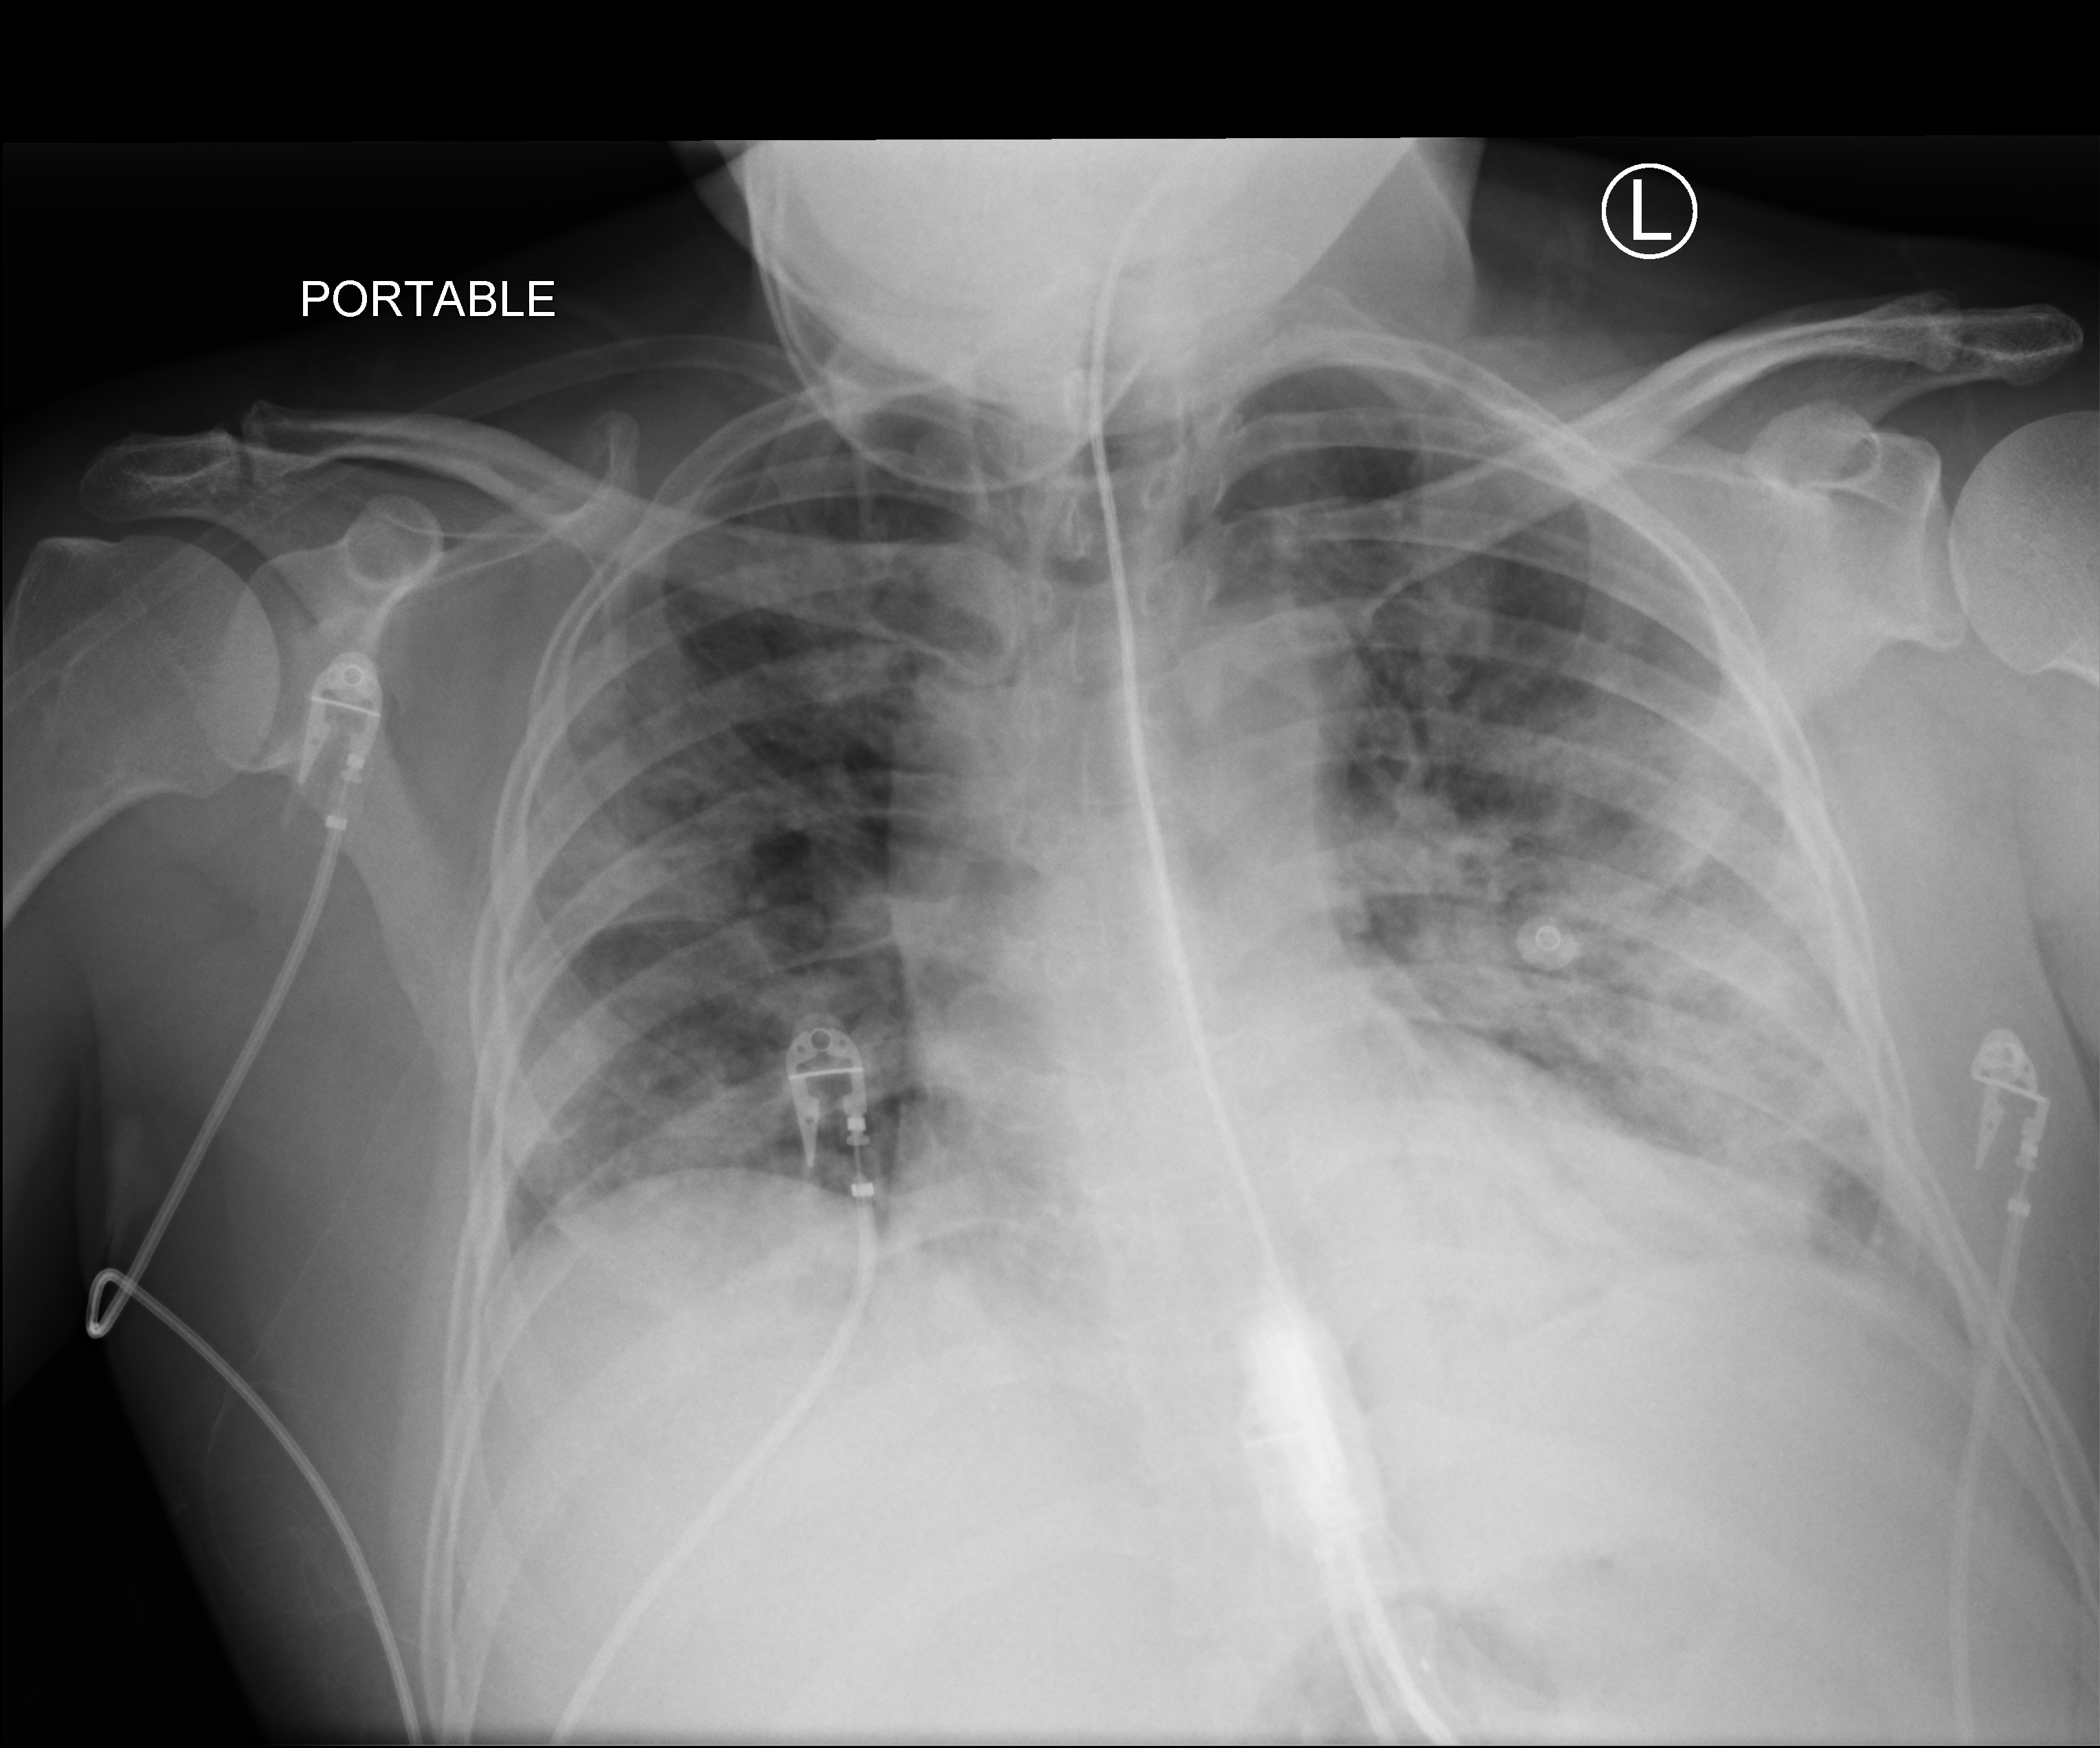
Portable chest radiograph, anteroposterior (AP) projection. Patient hospitalised with COVID-19; male, aged 18–59 years.
Hospital-stay facts (about this admission, not read from this image; timing relative to this image not recorded): mechanically ventilated during this hospital stay: no.